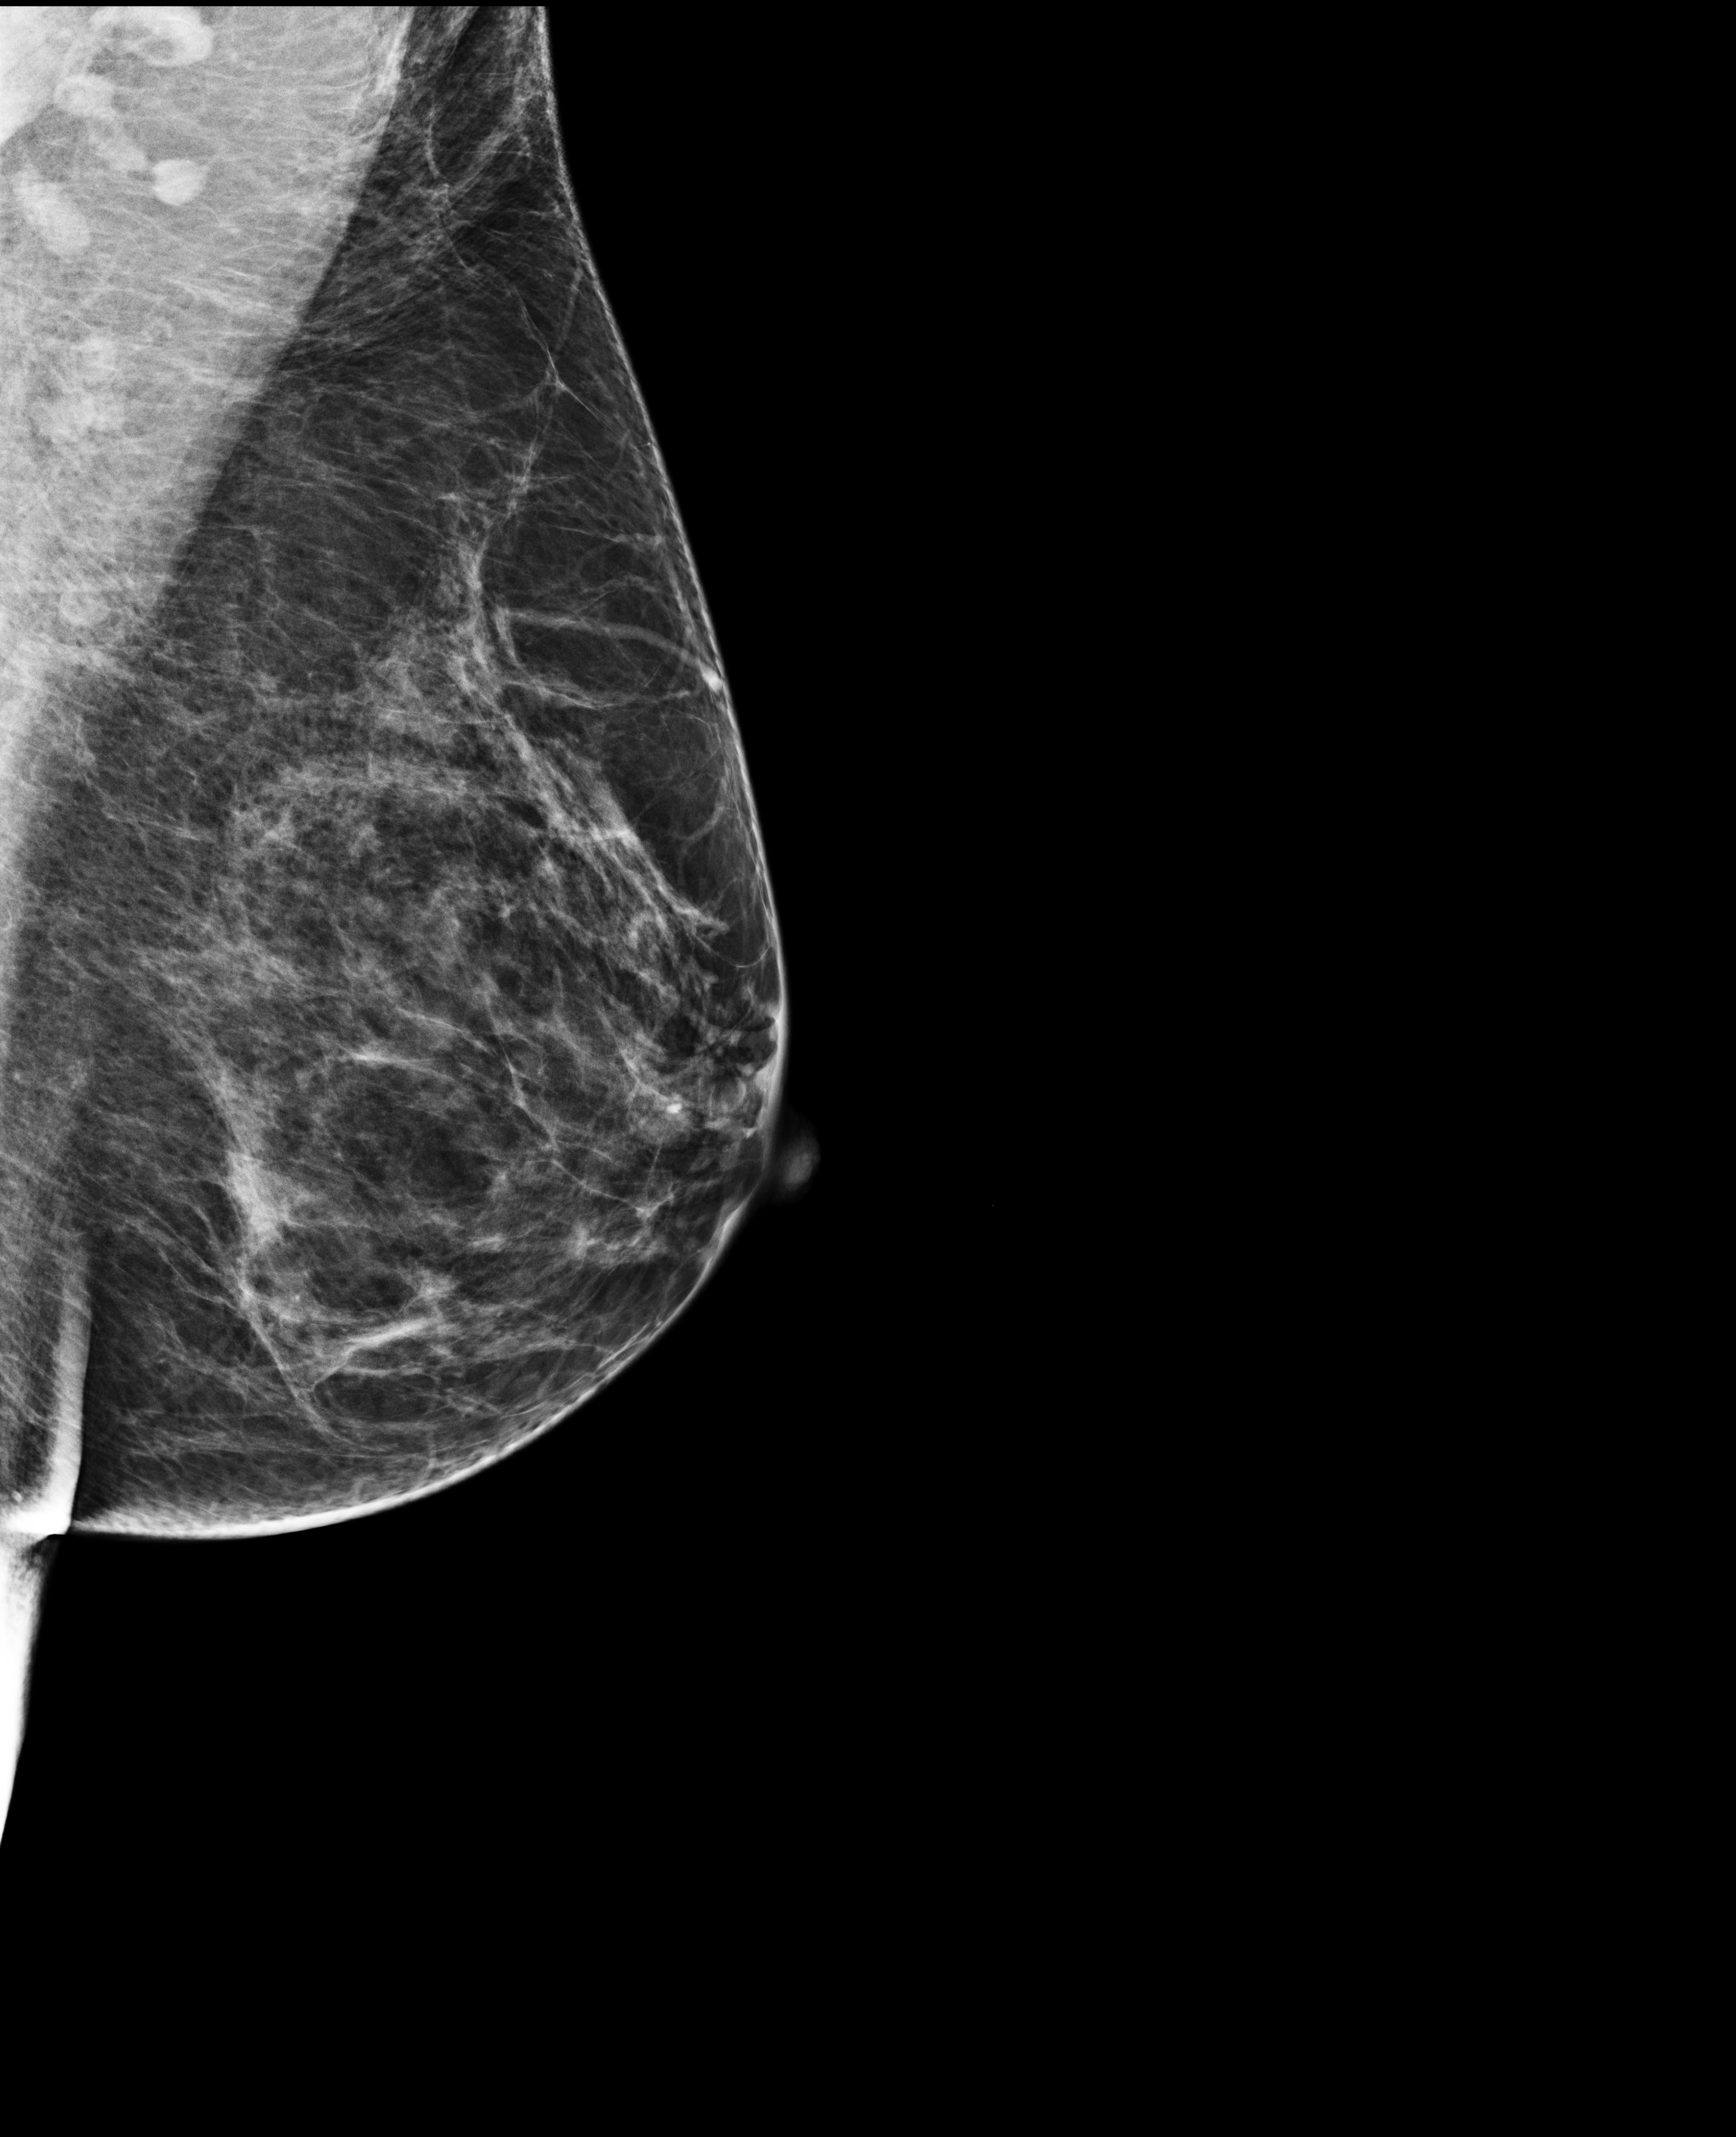
Screening examination; compressed breast thickness 65 mm; system: Selenia Dimensions. Patient aged 52 years (female).
Image type: full-field digital mammogram. Breast: left. Projection: MLO view.